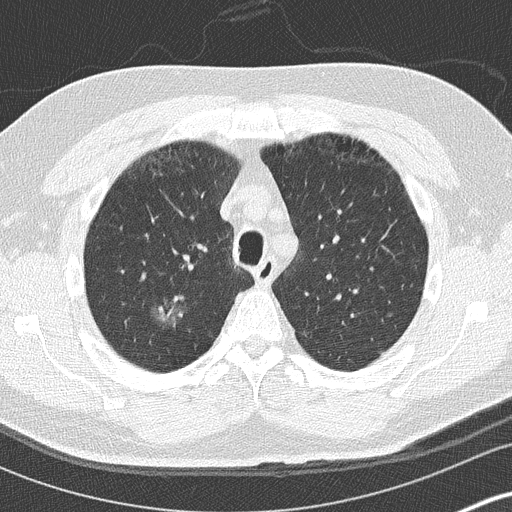
Low-dose screening chest CT, axial slice, first (baseline) screen, lung window (W 1500 / L -600 HU), 2 mm slice thickness, 120 kVp, slice 37 of 136 in the series. Male, age 59 years at enrolment. Current smoker at enrolment.
Lesion marked by an expert reader, bounding box [x1, y1, x2, y2] px = [146, 289, 200, 343]. Reader record for this screening exam (exam-level; its link to the box is not recorded): non-calcified nodule or mass ≥4 mm, right upper lobe, 16 × 16 mm, ground glass attenuation.